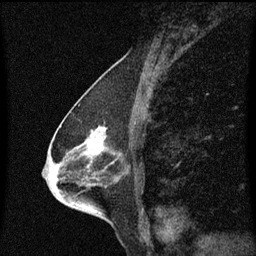
Breast MRI (dynamic contrast-enhanced), one sagittal slice; position 31 of 60 along the scan axis; dynamic contrast-enhanced series, image 2 of 3 at this slice position (ordered by acquisition); 1.5 T; TE 4.2 ms, TR 8.4 ms; 256 × 256 image matrix. Female patient, age 68 years. Case-level facts recorded for this patient, not image findings: setting: breast cancer imaged before/during neoadjuvant chemotherapy; receptor status: triple-negative.
Annotated regions visible in this slice (semi-automatically segmented with operator editing):
- analysis volume of interest (the breast-tissue region the enhancement analysis was run in; not a lesion): bounding box [x1, y1, x2, y2] px = [40, 114, 132, 203]
- tumour enhancement mask (voxels above the 70 % enhancement threshold inside the analysis volume of interest): [55, 128, 104, 179]